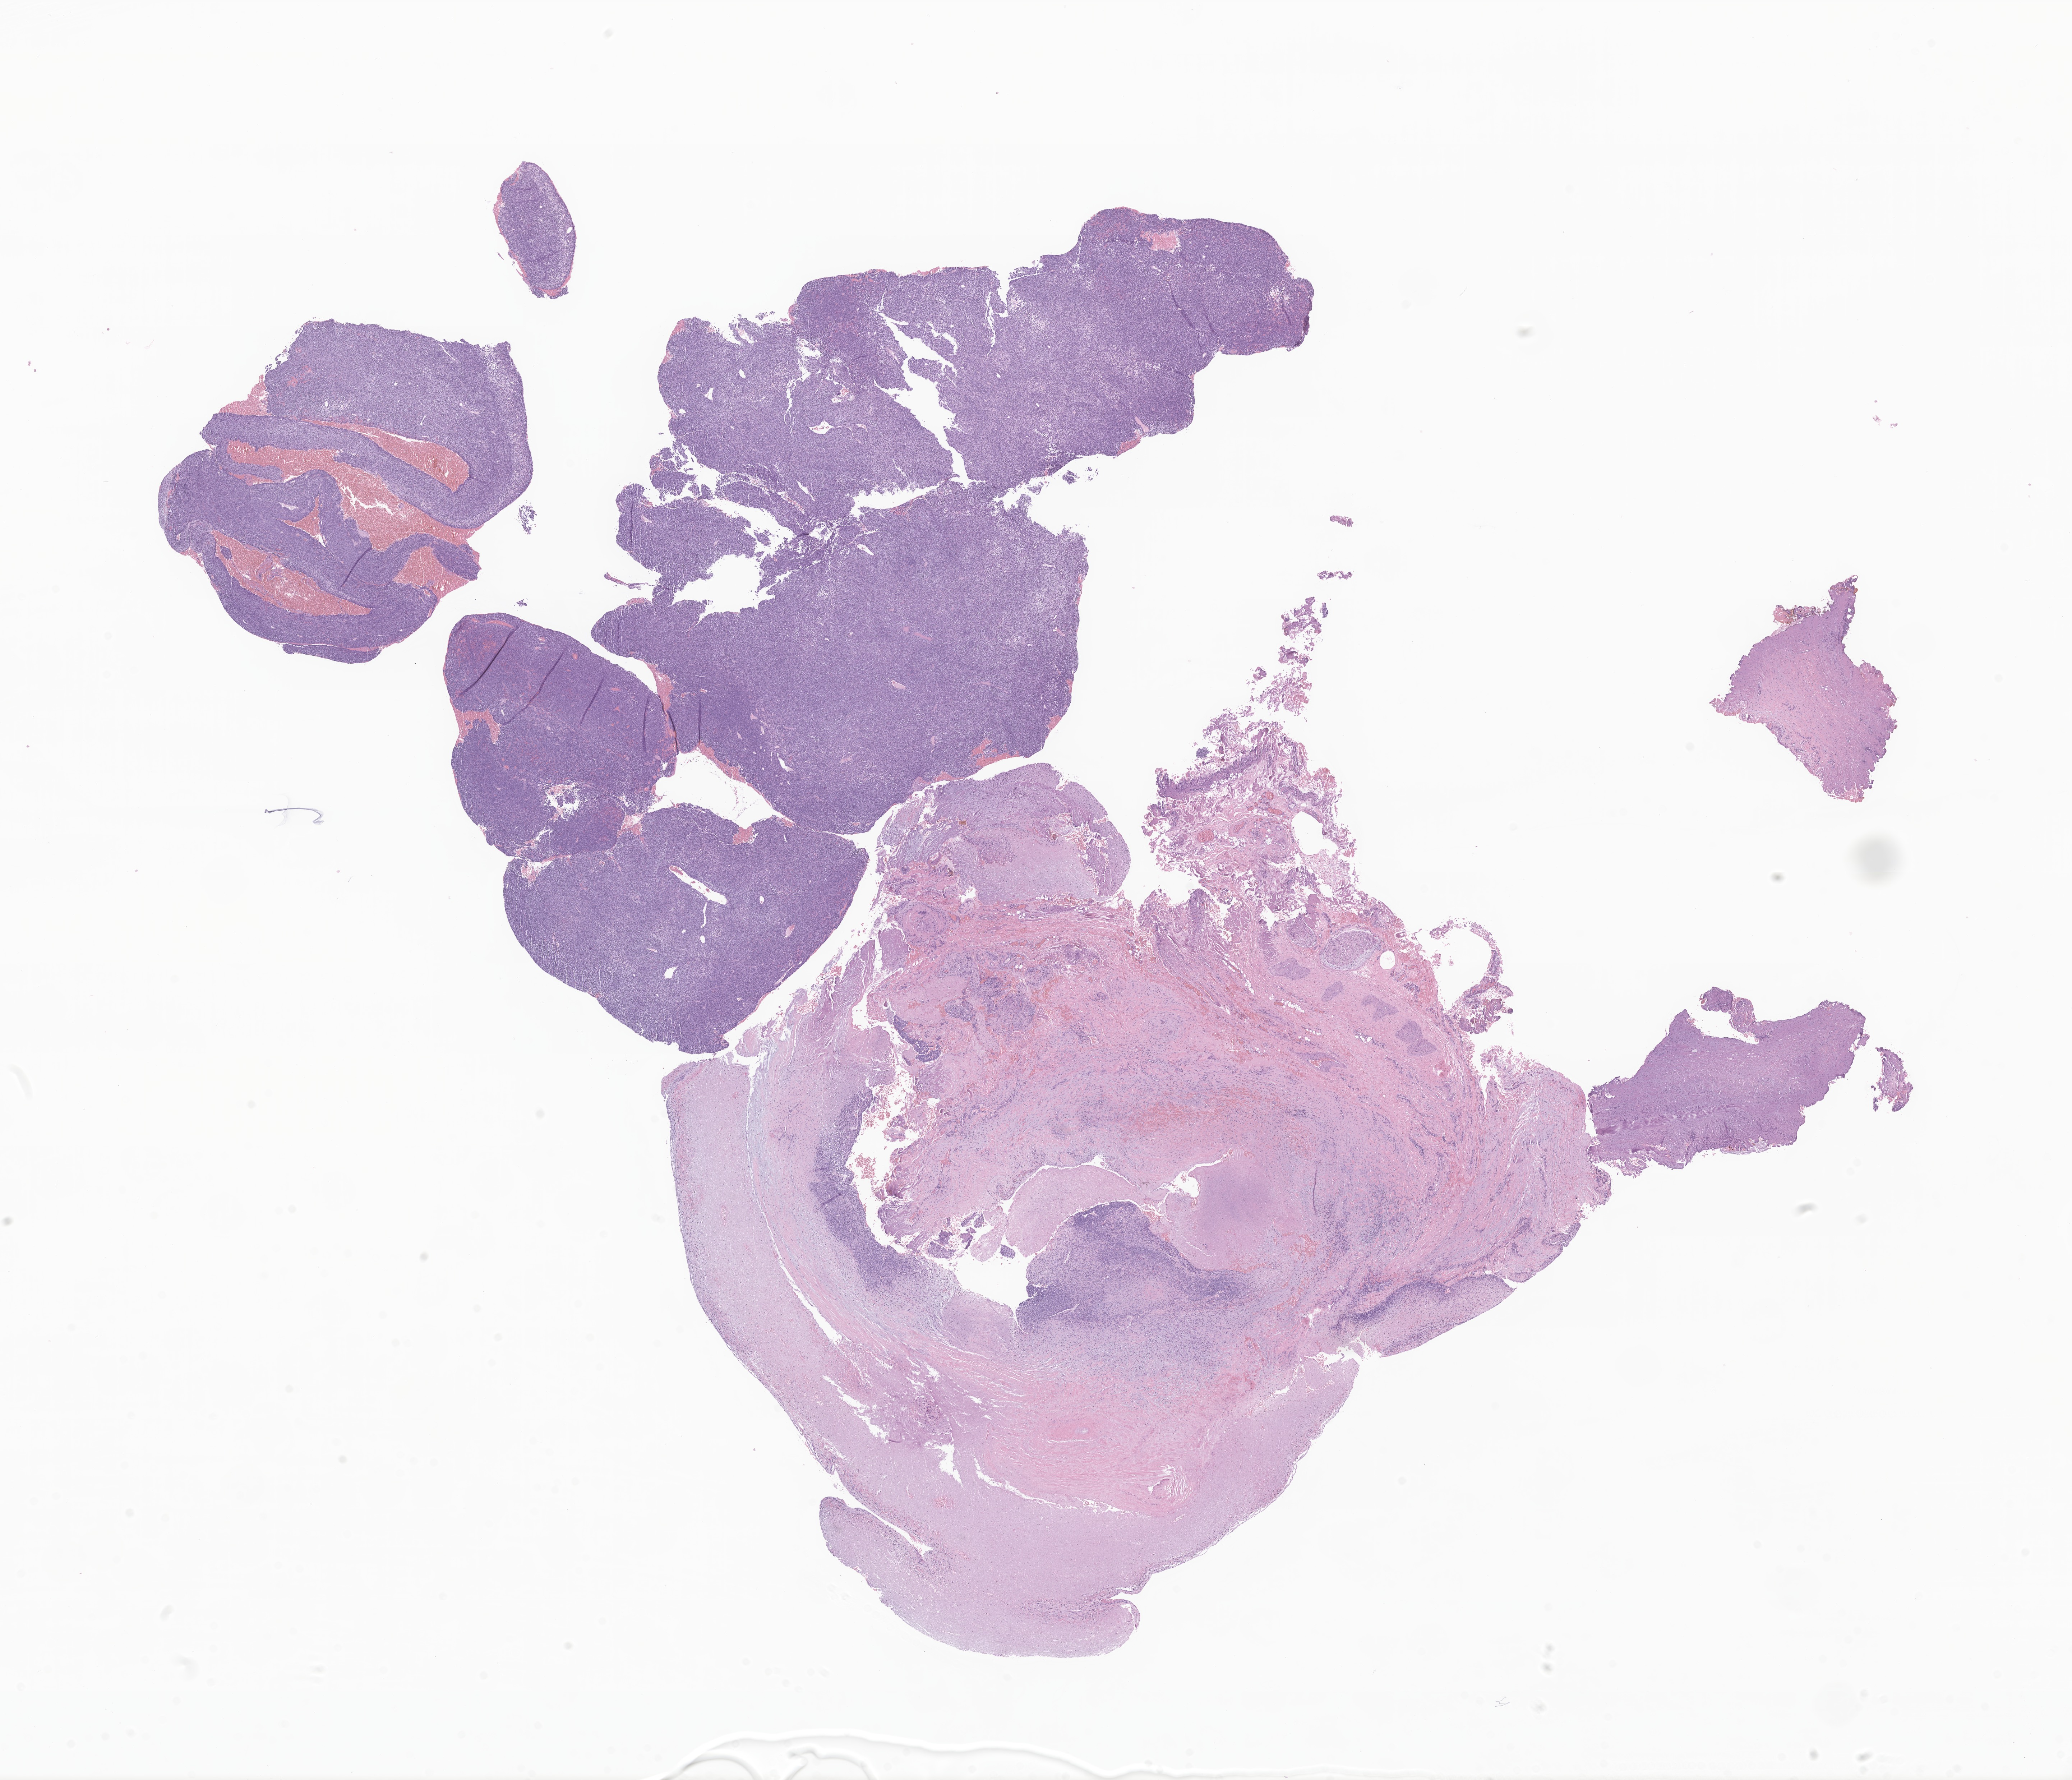
Hematoxylin and eosin (H&E) whole-slide image of tumor tissue from the soft tissue, whole scanned area (about 24.3 x 20.9 mm) shown as a low-resolution overview. Formalin-fixed, paraffin-embedded (FFPE) tissue. Patient female; age 71 months (5 years 11 months).
Recorded diagnosis: Synovial sarcoma, NOS.